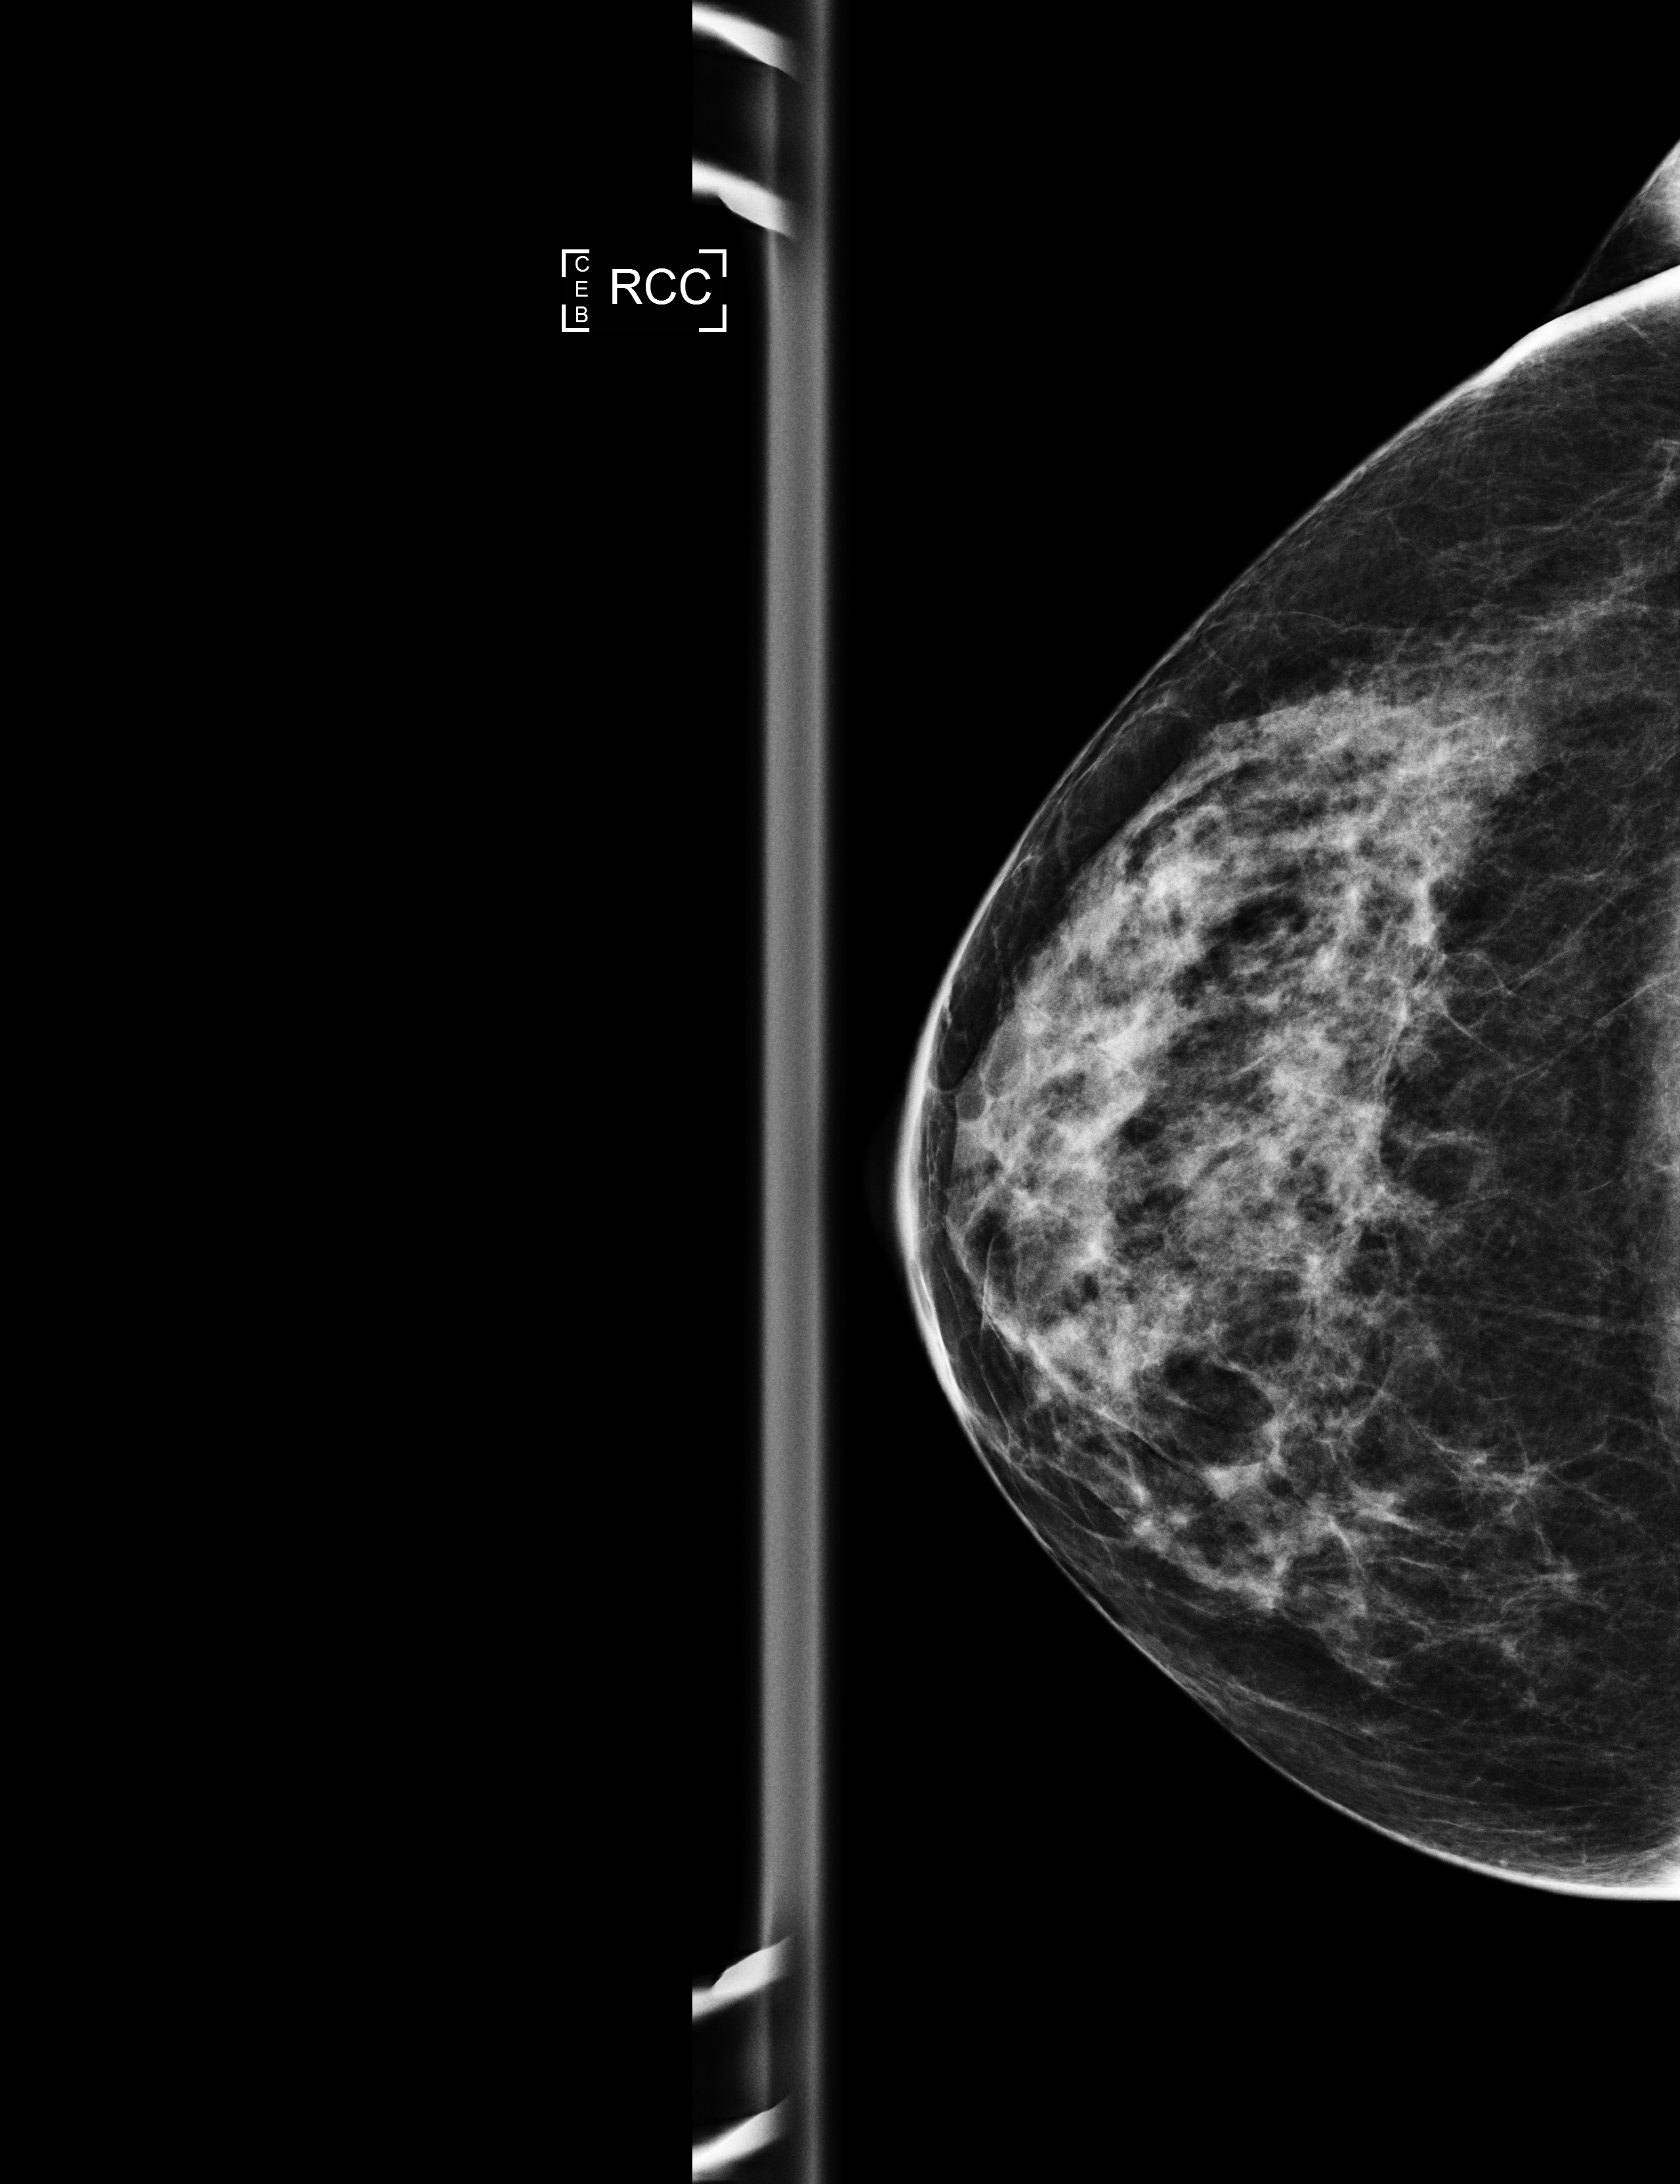
Full-field digital mammogram (FFDM); right breast; CC view; annual screening mammography examination. Patient: female, 68 years.
Final BI-RADS category for the screening round (tomosynthesis exam, both breasts): category 2.